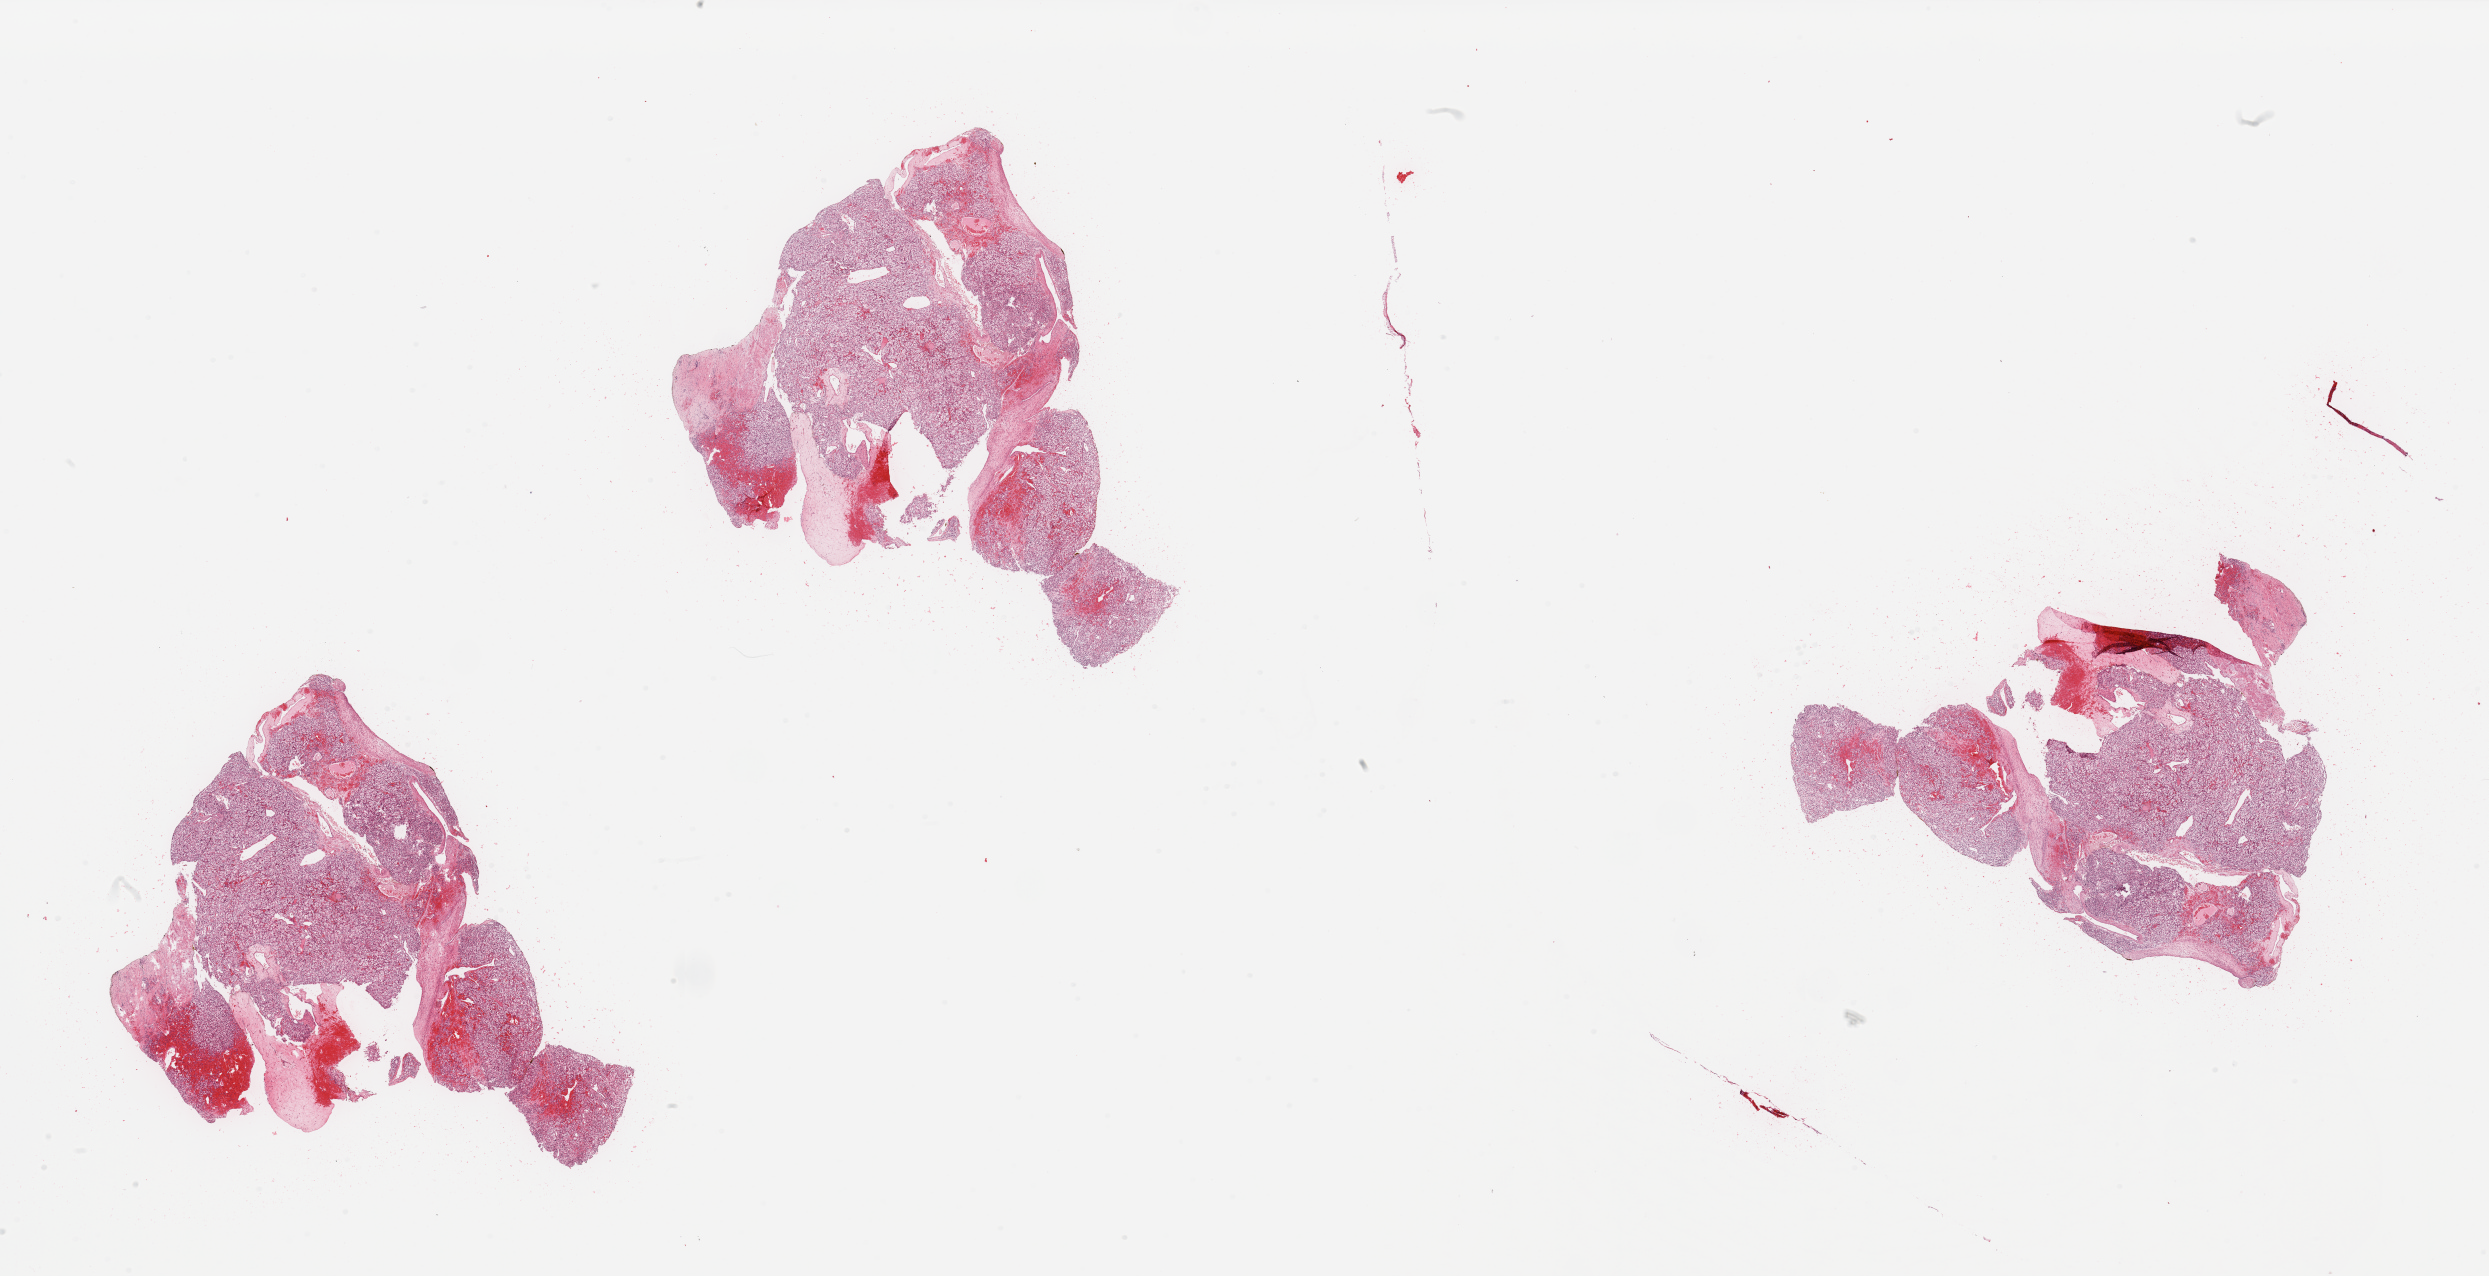
H&E whole-slide image — whole scanned area (about 39.4 x 20.2 mm, slide scanned at 20x) shown as a low-resolution overview. Tumour tissue sample, sampled site: kidney. Patient: male, age 62 years. Histologic grade: G3 (poorly differentiated). Composition of this section per pathologist review: tumour nuclei 85%, necrosis 2%.
Primary tumour site (as recorded): lower pole. Diagnosis: Renal cell carcinoma, NOS.